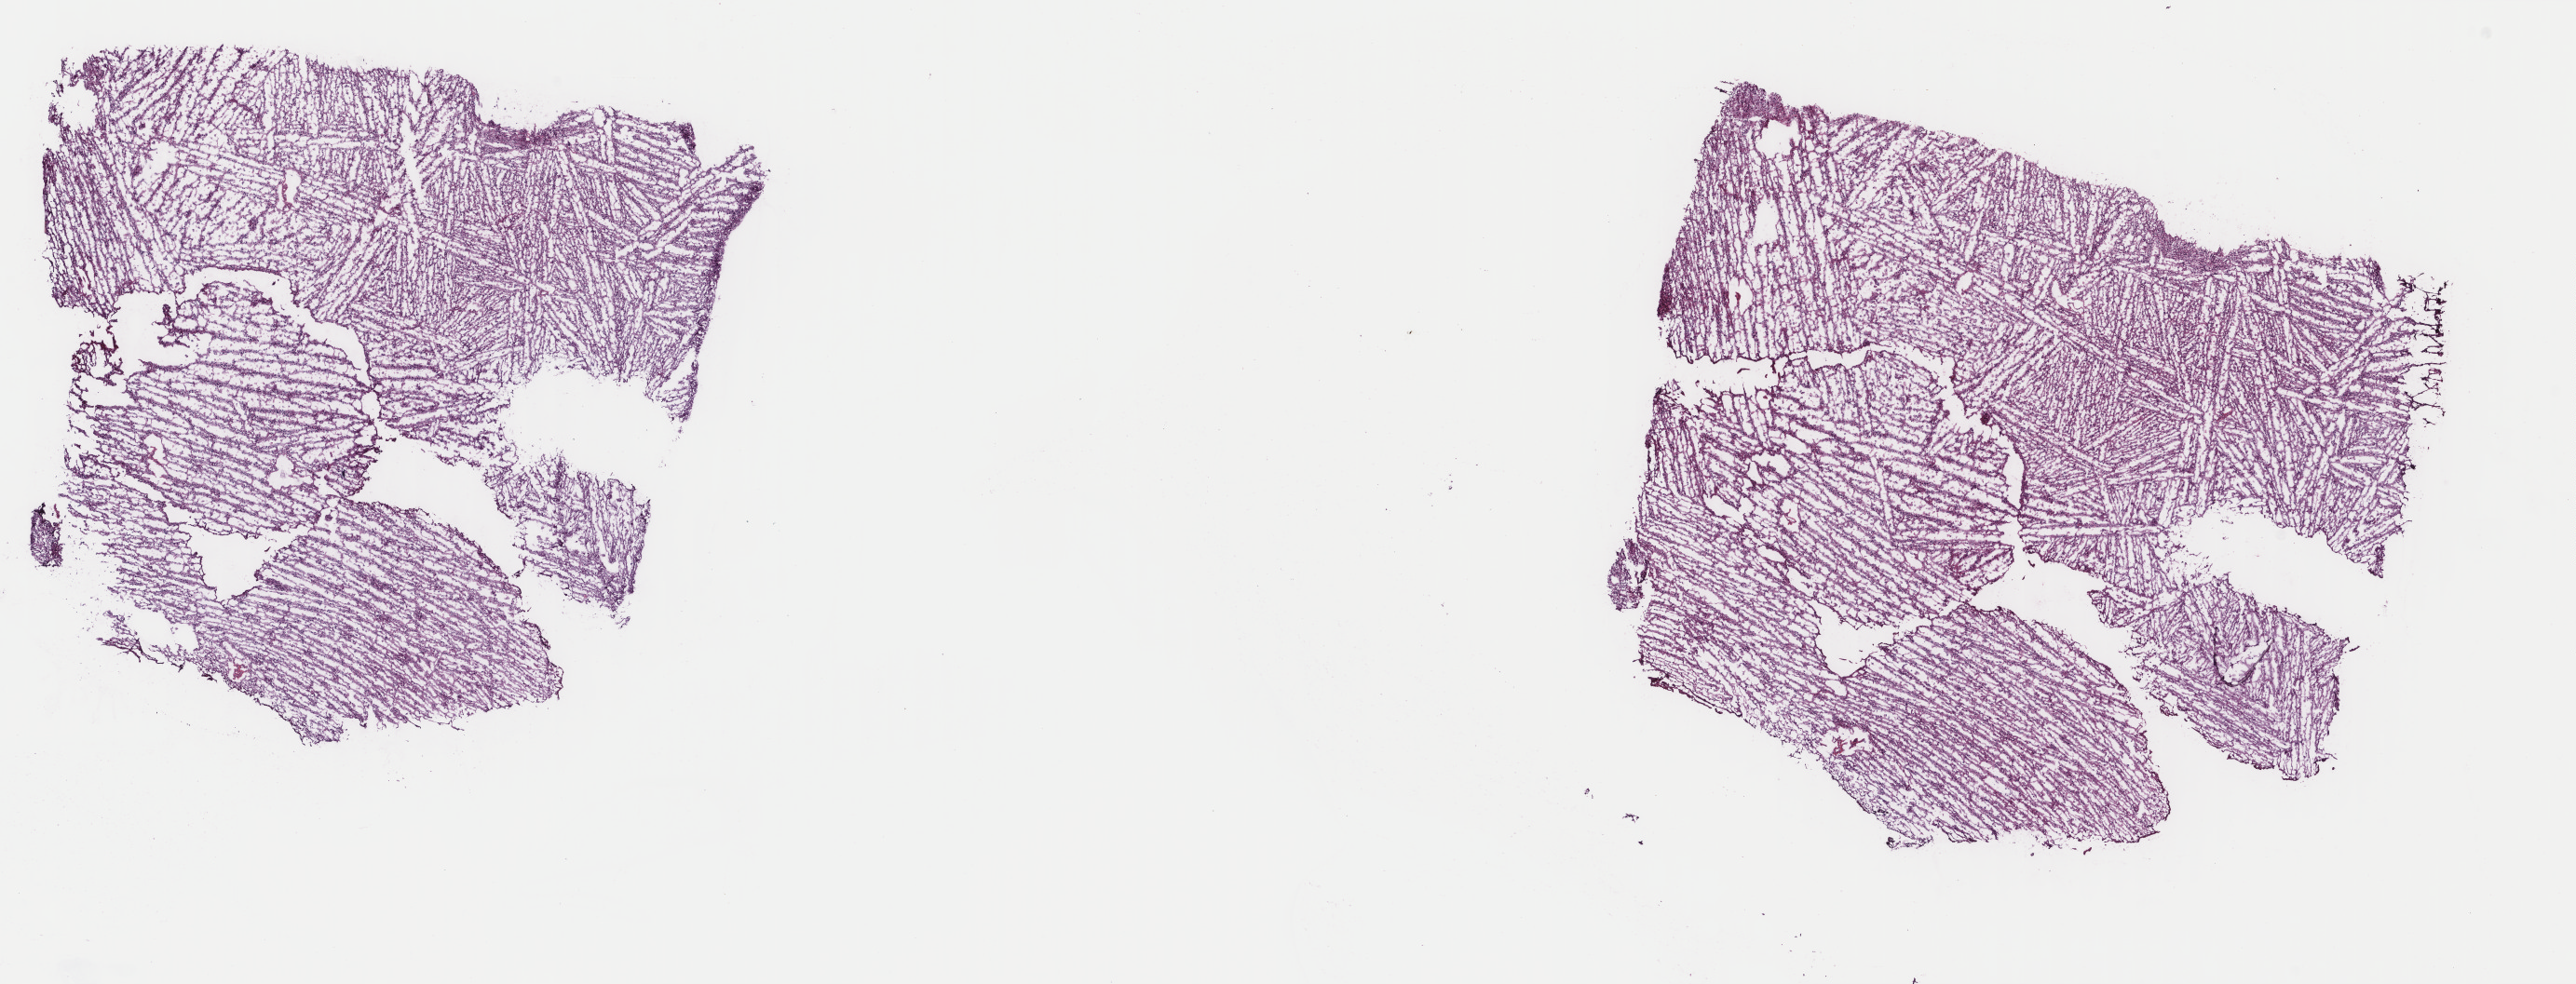
Digitized Hematoxylin and eosin (H&E) stained tissue section (whole slide) — low-resolution overview of the scanned area, about 22.0 x 8.4 mm (slide scanned at 40x); frozen section from the top of the tissue portion; sample: primary tumour, brain. Patient: male, age at initial diagnosis 35 years. Histologic grade: G3 (poorly differentiated). Slide review estimates, as recorded: tumour cells 60%, tumour nuclei 85%, normal cells 5%, stromal cells 35%, necrosis 0%. Infiltration values recorded for this section: lymphocyte infiltration 0%, monocyte infiltration 0%, neutrophil infiltration 0%.
- histologic diagnosis: Astrocytoma, anaplastic (cerebrum)